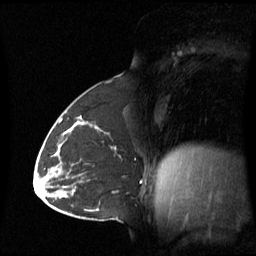
Breast MRI (dynamic contrast-enhanced), one sagittal slice. Slice 31 of 60 in the series (ordered by position). Dynamic contrast-enhanced series, image 2 of 3 at this slice position (ordered by acquisition). 1.5 T. TE 4.2 ms, TR 8.4 ms. 2.8 mm slice thickness. 256 × 256 image matrix, field of view 270 × 270 mm. Female patient, age 43 years. Case-level facts recorded for this patient, not image findings: setting: breast cancer imaged before/during neoadjuvant chemotherapy; receptor status: triple-negative.
Structures marked on this image (semi-automatically segmented with operator editing):
- analysis volume of interest (the breast-tissue region the enhancement analysis was run in; not a lesion): bounding box [x1, y1, x2, y2] px = [62, 124, 116, 180]
- tumour enhancement mask (voxels above the 70 % enhancement threshold inside the analysis volume of interest): [62, 124, 97, 135]